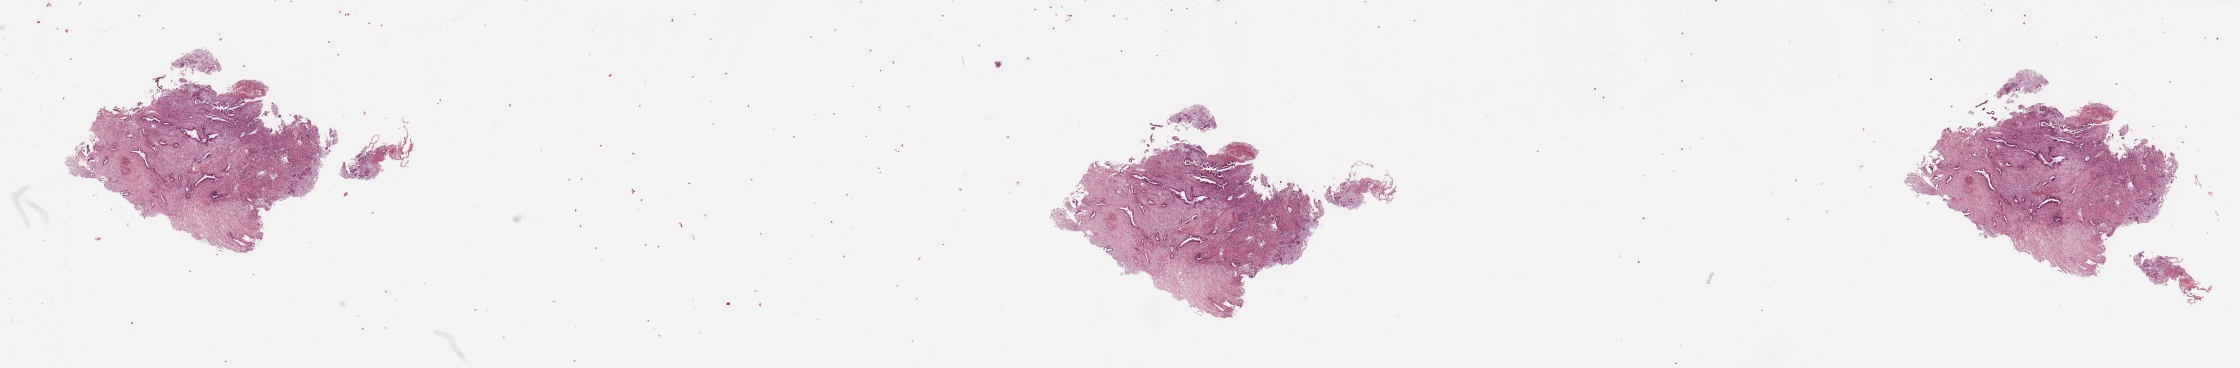
Digitized H&E-stained tissue section (whole slide), shown as a low-resolution overview of the whole scanned area (about 35.4 x 5.8 mm, acquisition: 20x scan); pancreas, tumour tissue. Female, 53 y/o. Histologic grade: G2 (moderately differentiated).
* primary tumour site (as recorded): head
* AJCC pathologic stage: III
* histologic diagnosis: Infiltrating duct carcinoma, NOS